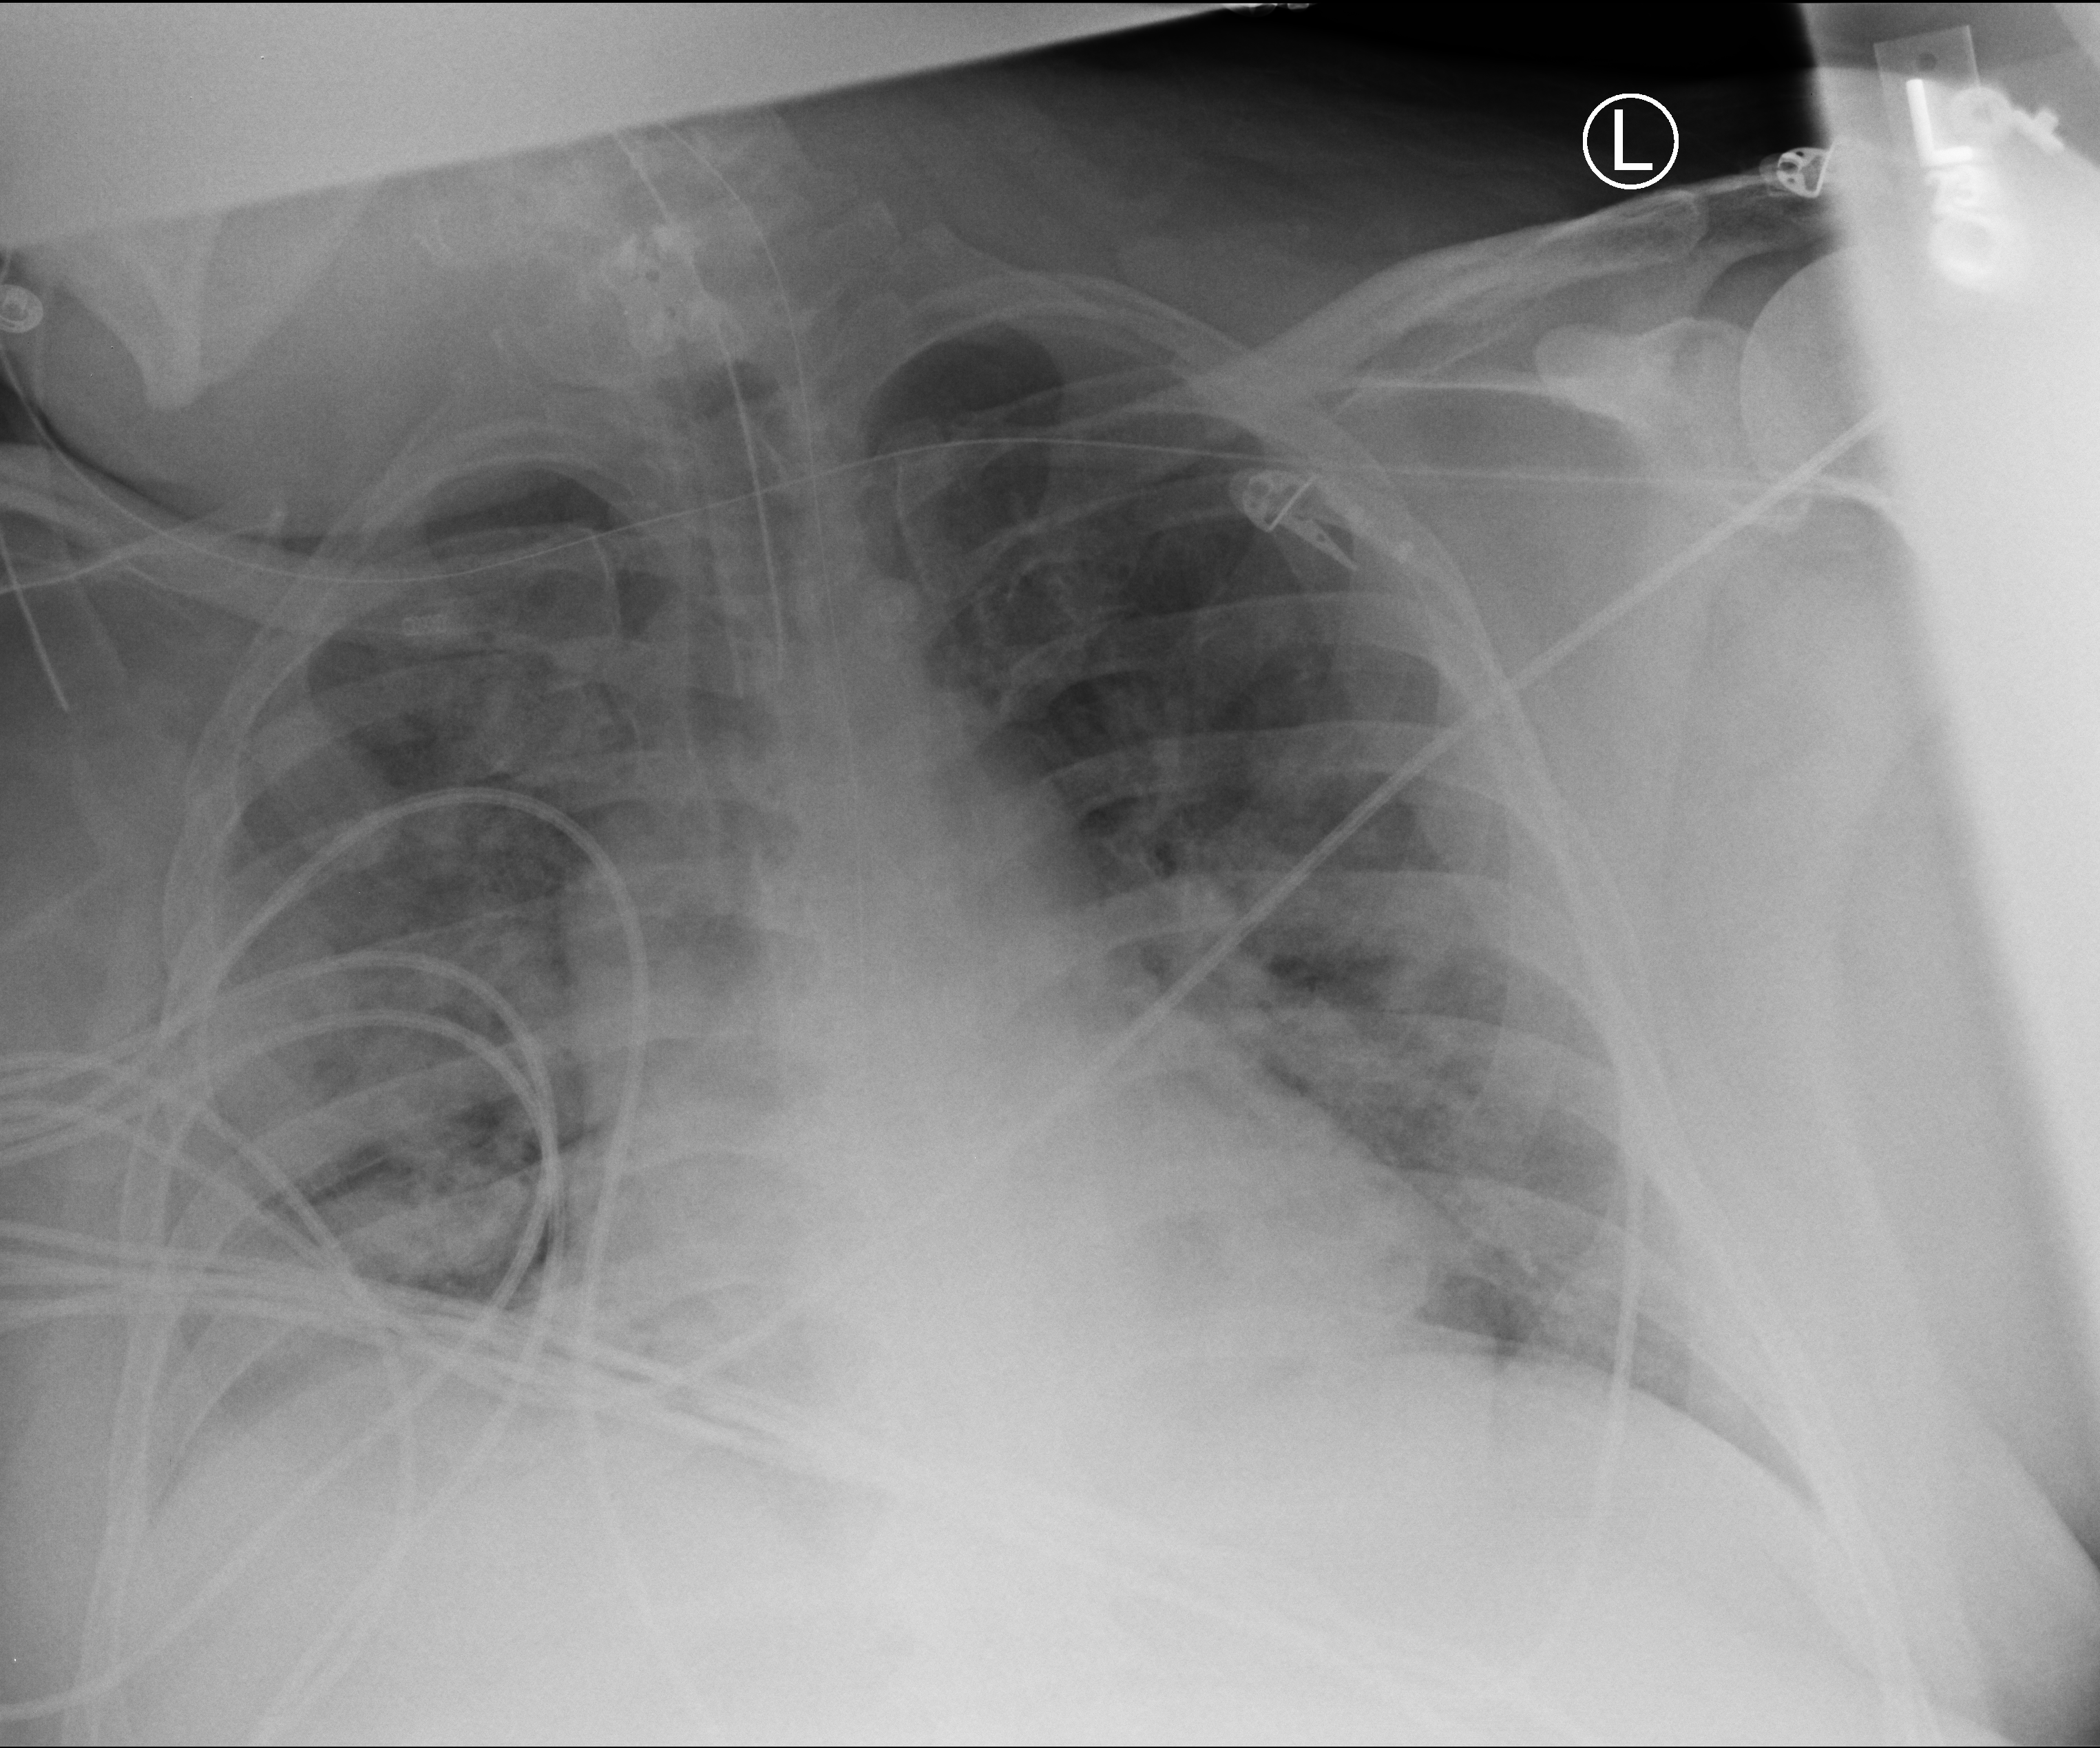
Portable chest radiograph; anteroposterior (AP) projection. Male patient hospitalised with COVID-19, age 18–59 years.
From the hospital-stay record, not from the radiograph (when in the stay this image was taken is not recorded):
- chronic kidney disease (admission record): no